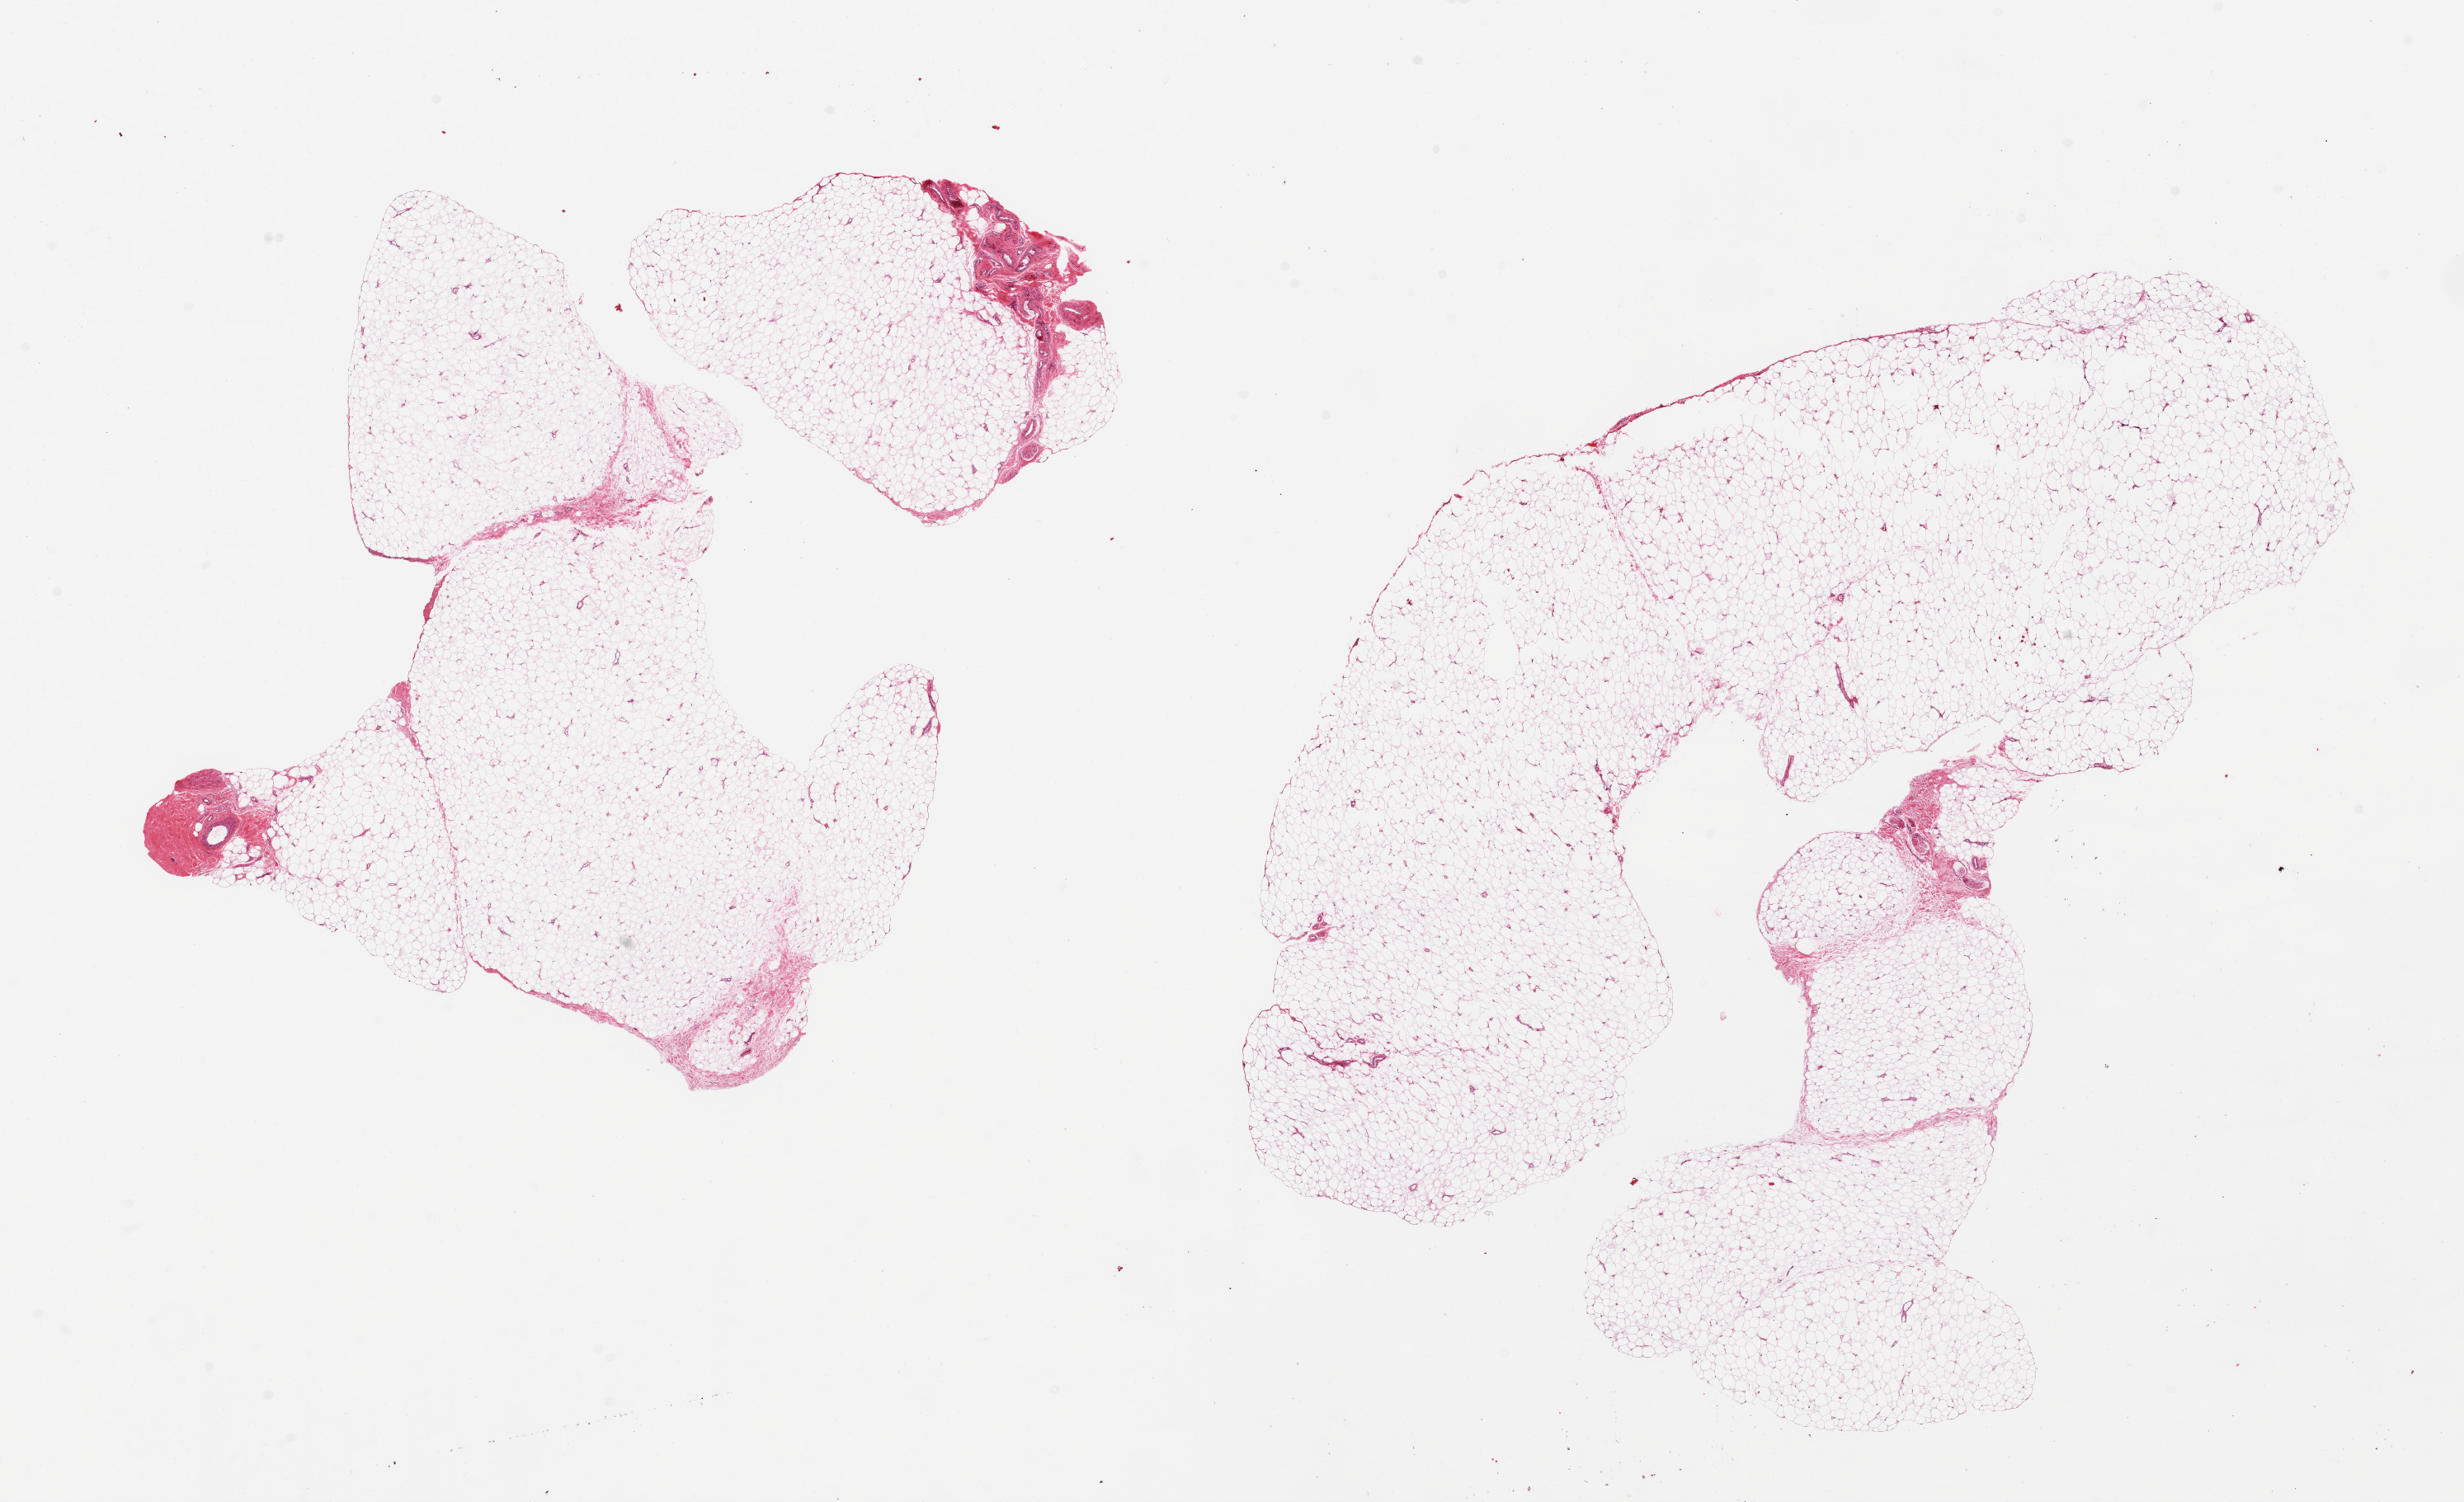
Digitized hematoxylin and eosin (H&E)-stained section, brightfield, low-resolution overview of the scanned area, about 23.6 x 14.4 mm (slide scanned at 20x); PAXgene-fixed, paraffin-embedded tissue; target tissue: adipose tissue; tissue donor sample.
* pathologist's review note for this sample: 2 pieces; mature fat with small component of nerve/vessels